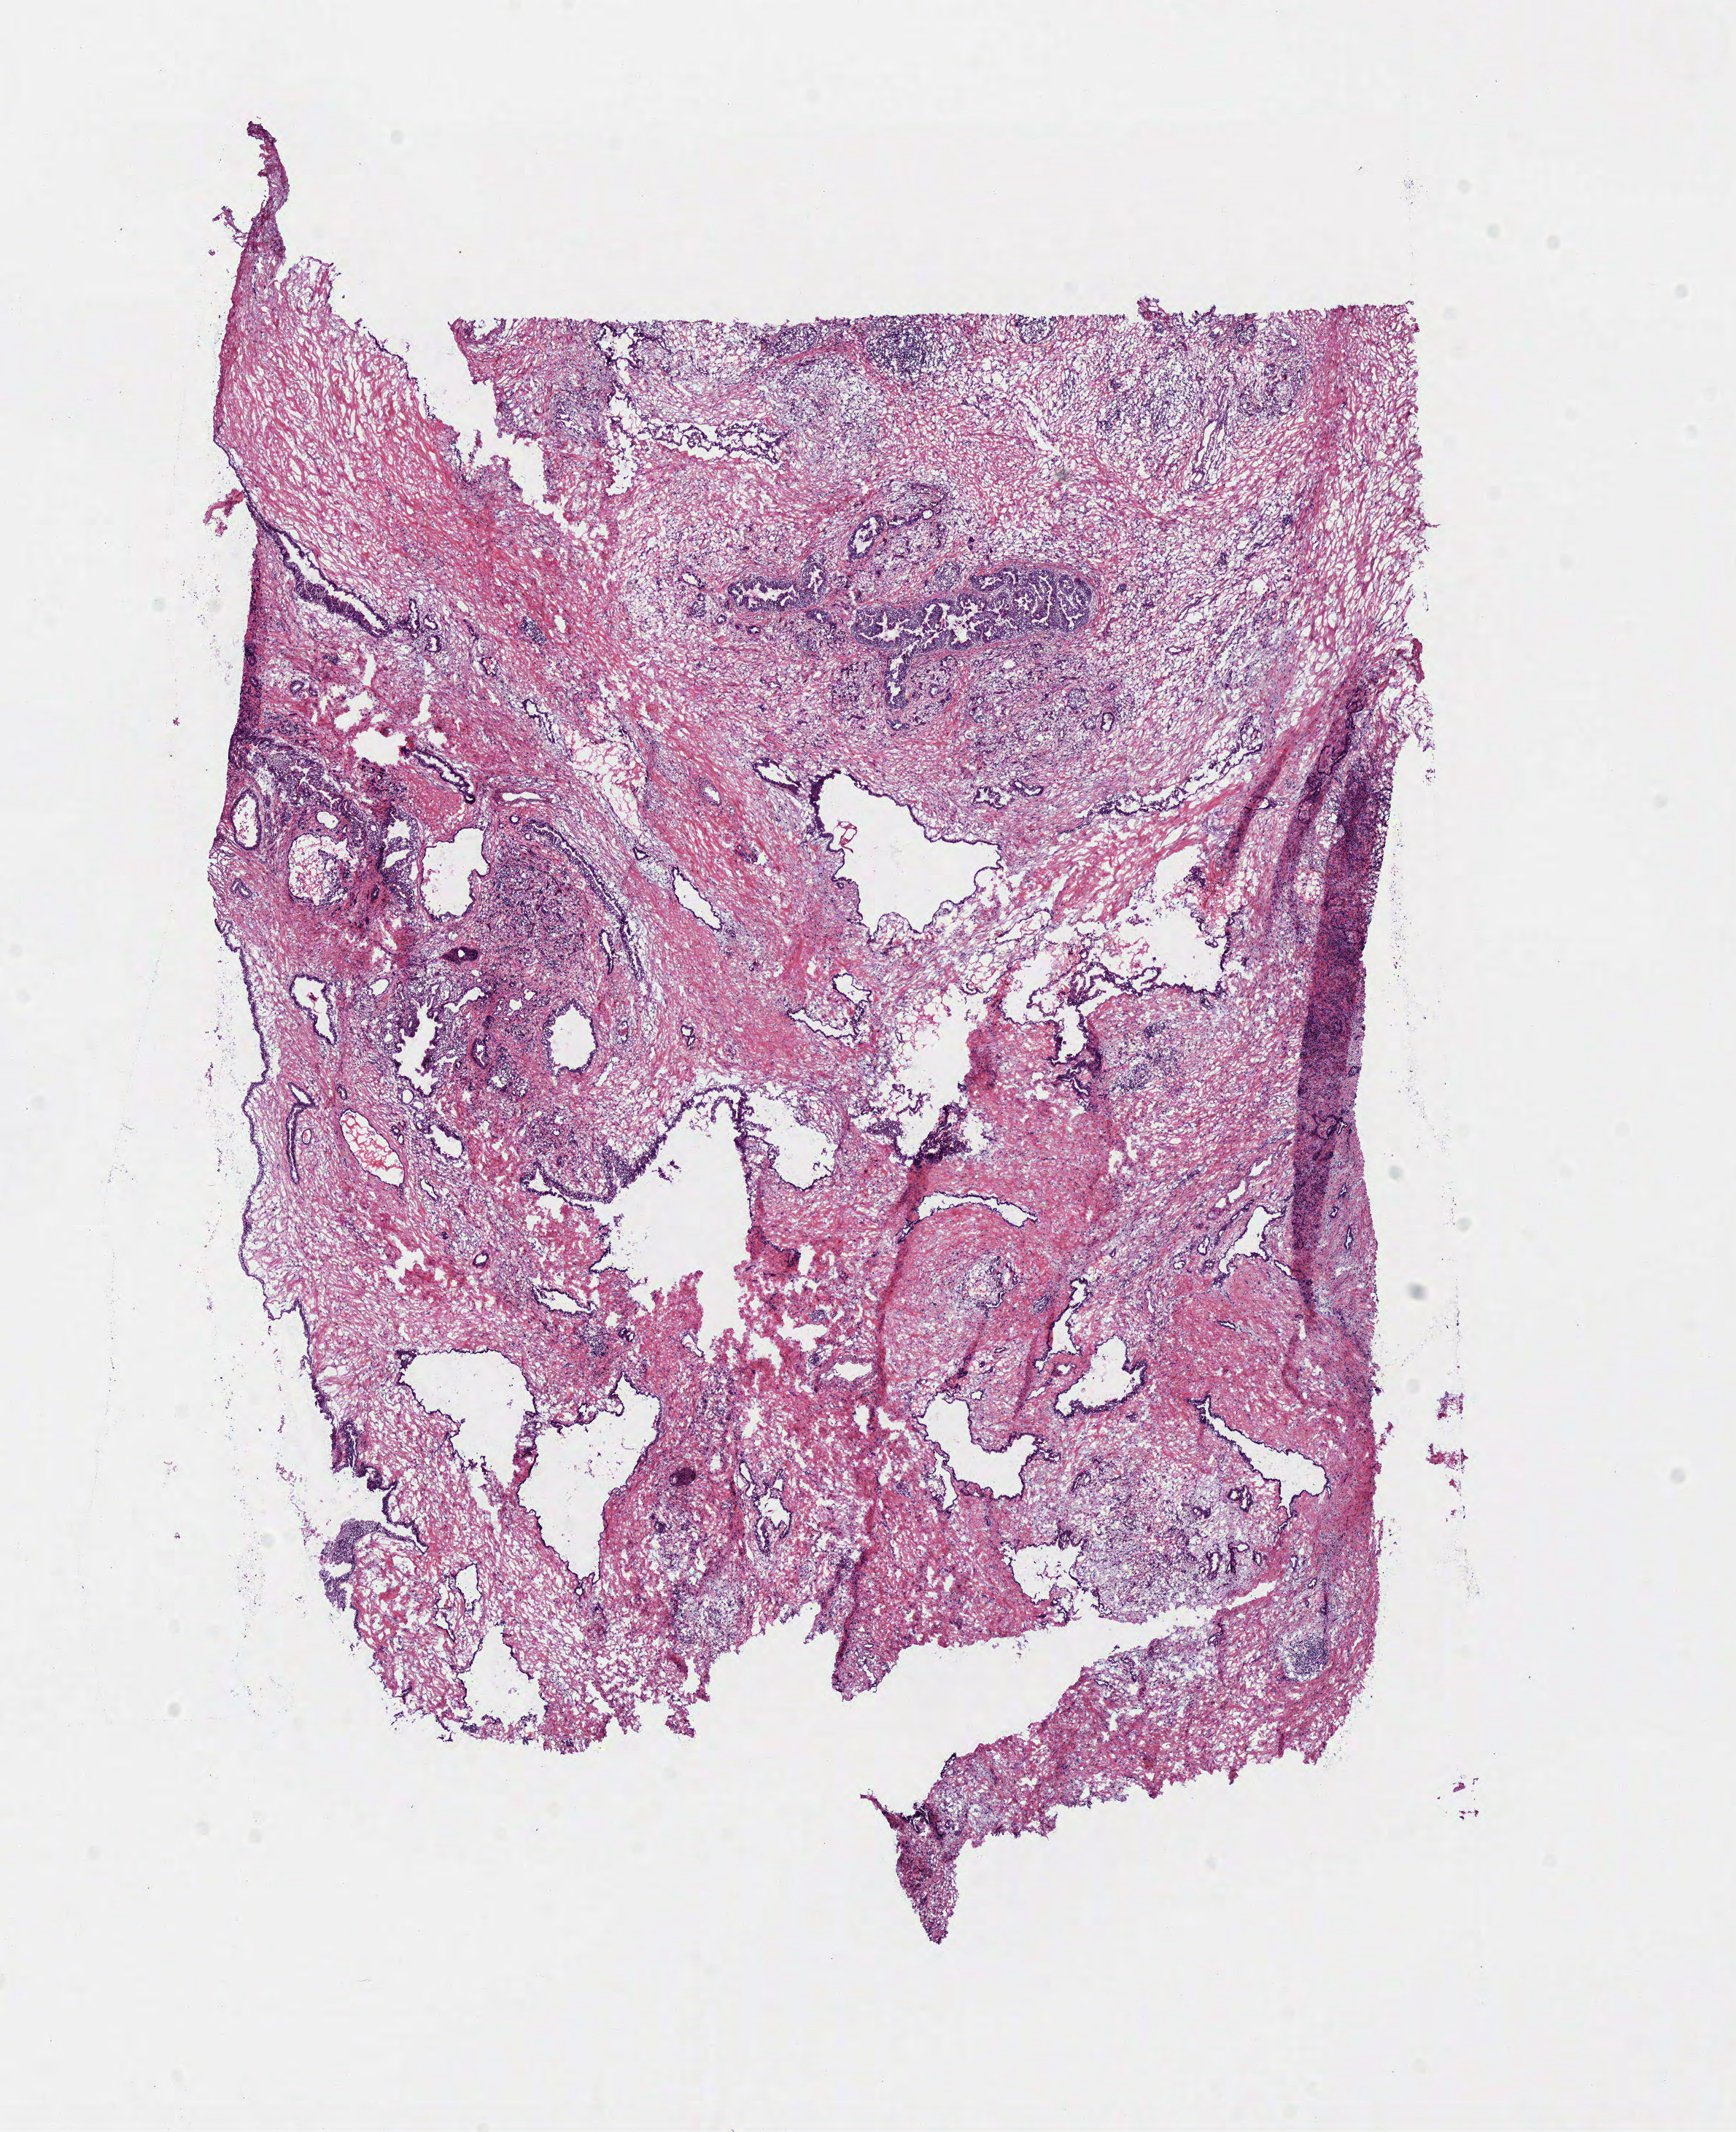
Whole-slide histology image, H&E-stained — low-resolution overview of the scanned area, about 9.4 x 11.5 mm (slide scanned at 40x); frozen section from the bottom of the tissue portion; primary tumour sample from the pancreas. Male, age 71 years at initial diagnosis. Histologic grade: G1 (well differentiated). Composition of this section per pathologist review: tumour cells 70%, tumour nuclei 70%, normal cells 0%, stromal cells 30%, necrosis 0%.
AJCC pathologic stage: IV (6th edition). Pathologic diagnosis: Infiltrating duct carcinoma, NOS (head of pancreas).